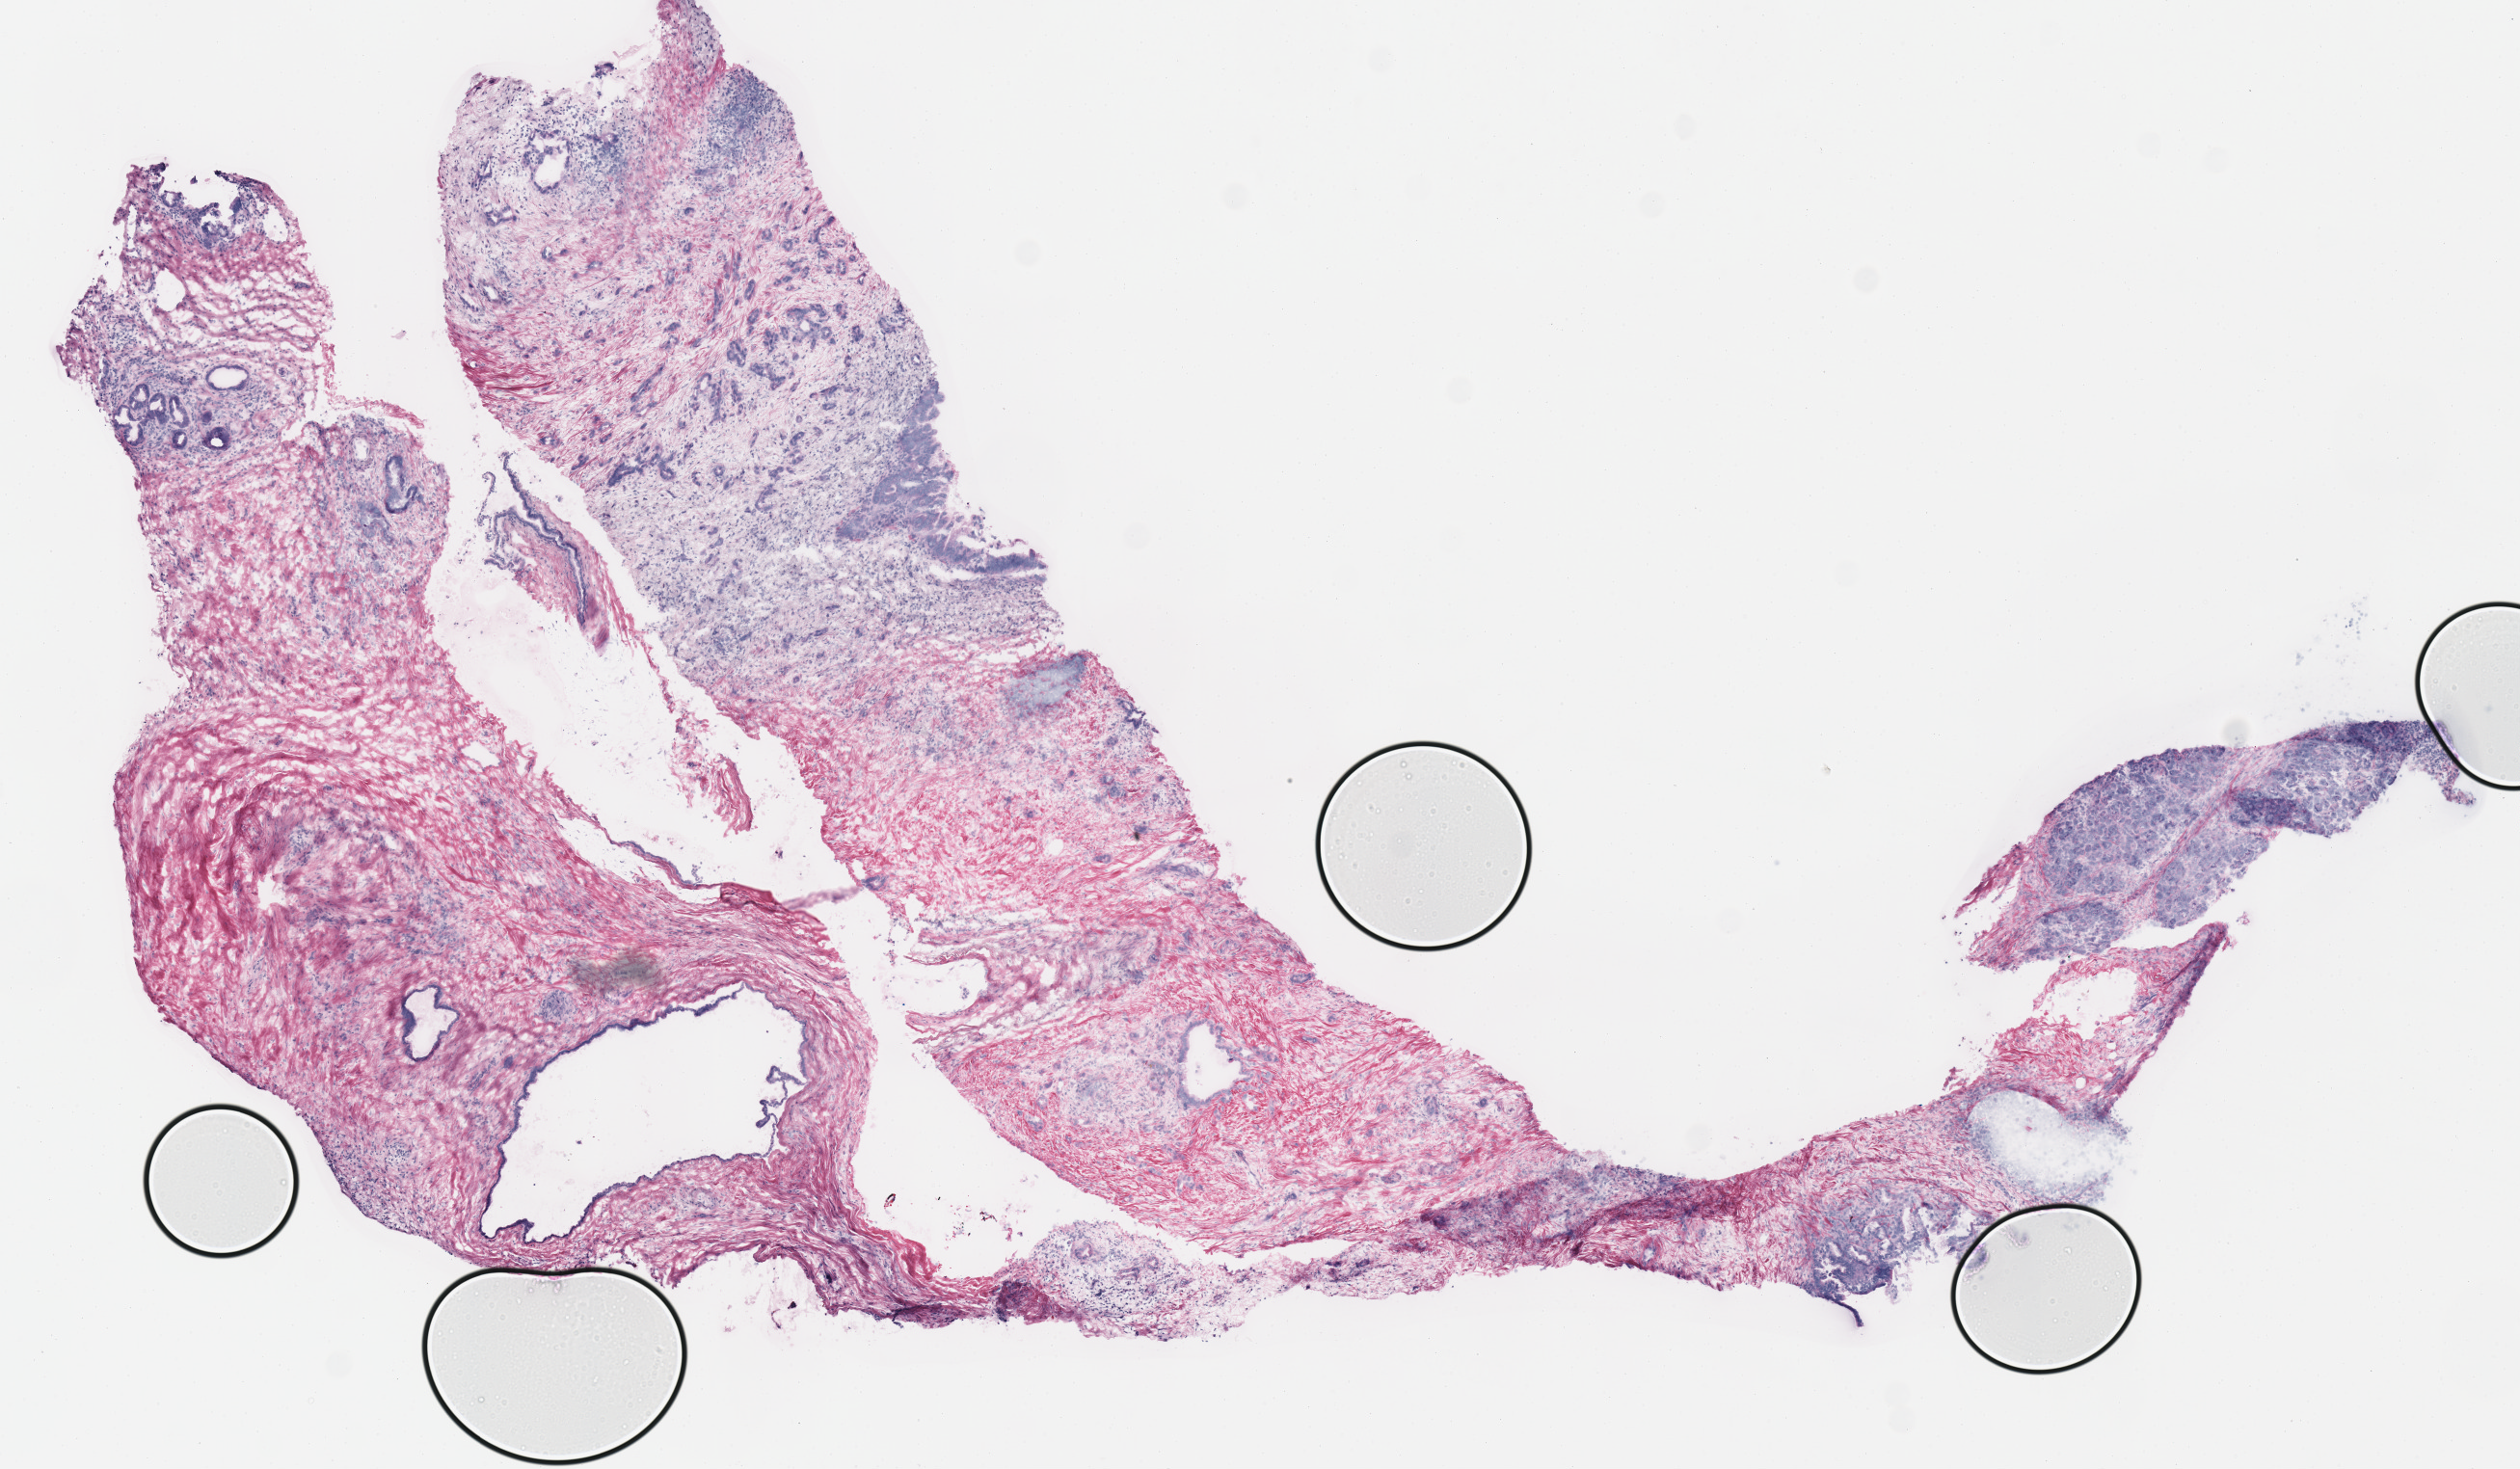
Whole-slide histology image, H&E-stained — low-resolution overview of the scanned area, about 10.3 x 6.0 mm (slide scanned at 40x). Frozen section from the top of the tissue portion. Pancreas, primary tumour sample. Female patient; age at initial diagnosis 85 years.
Diagnosis: Infiltrating duct carcinoma, NOS.